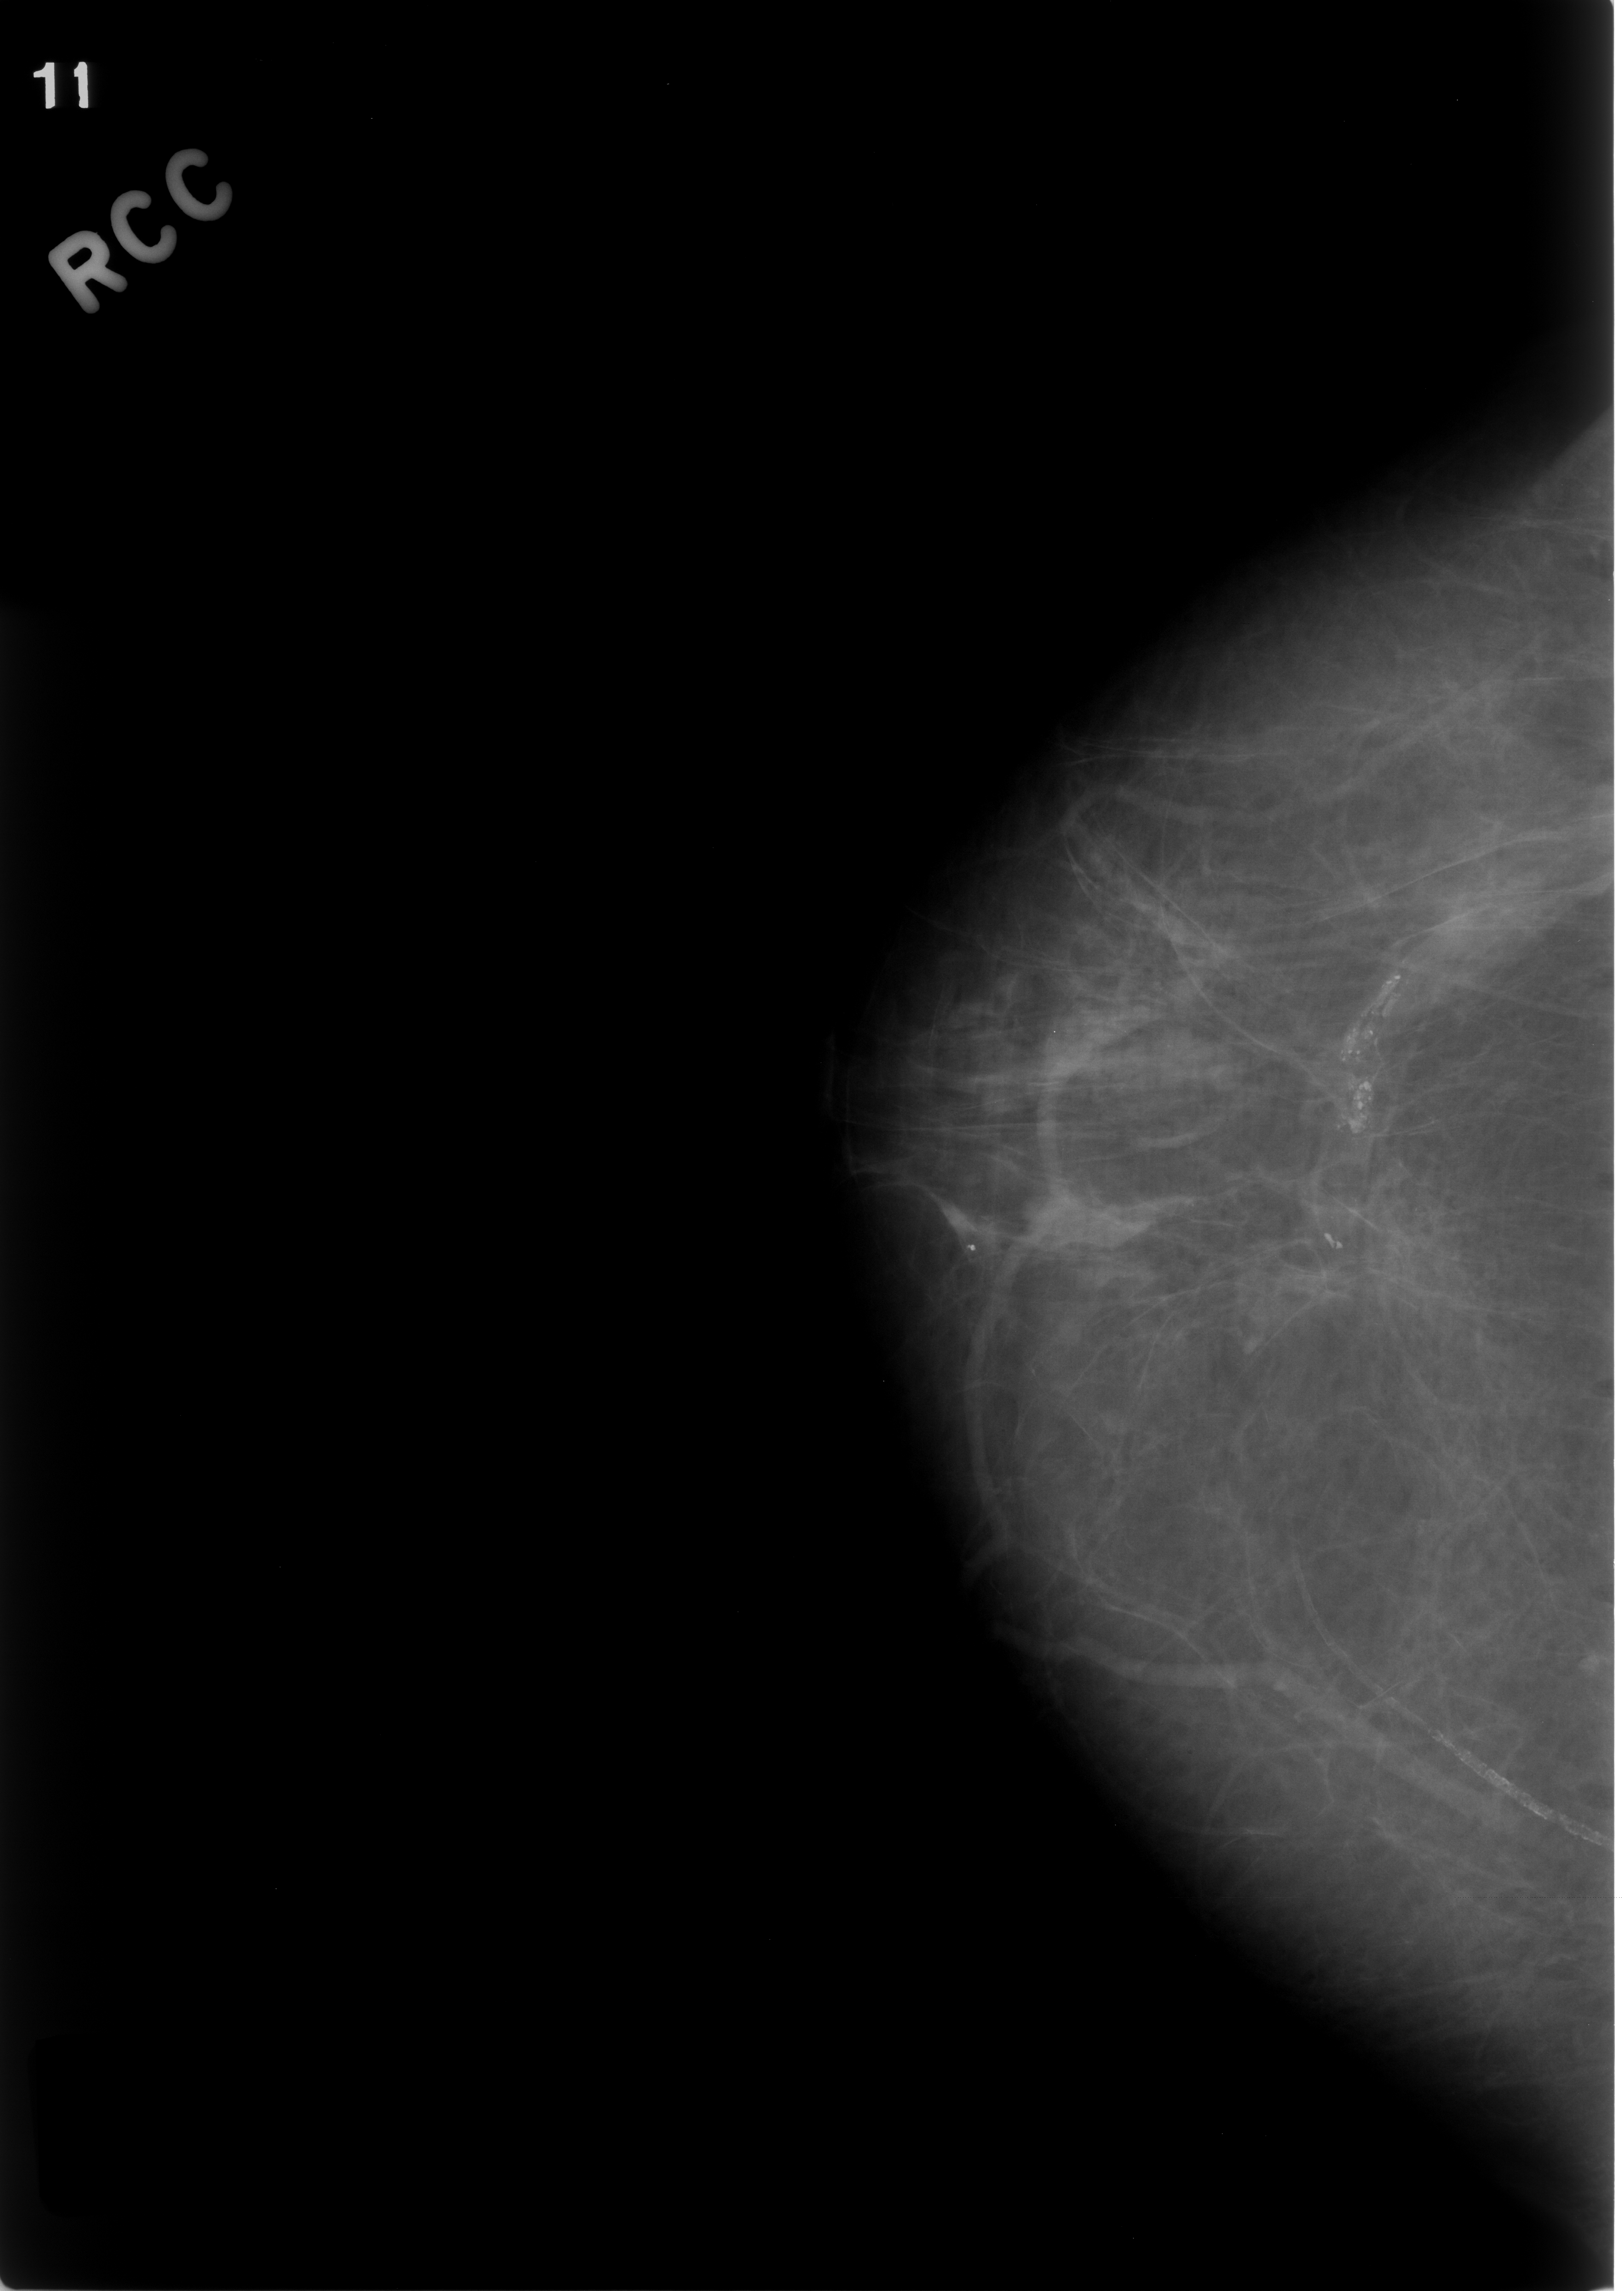
Mammogram (digitized film), right breast, CC view, BI-RADS breast density category 1 (scale 1–4).
Marked findings (only marked abnormalities are described; nothing is implied about the rest of the image): calcifications, morphology pleomorphic, distribution segmental; BI-RADS assessment category 4; pathology (as recorded): benign.